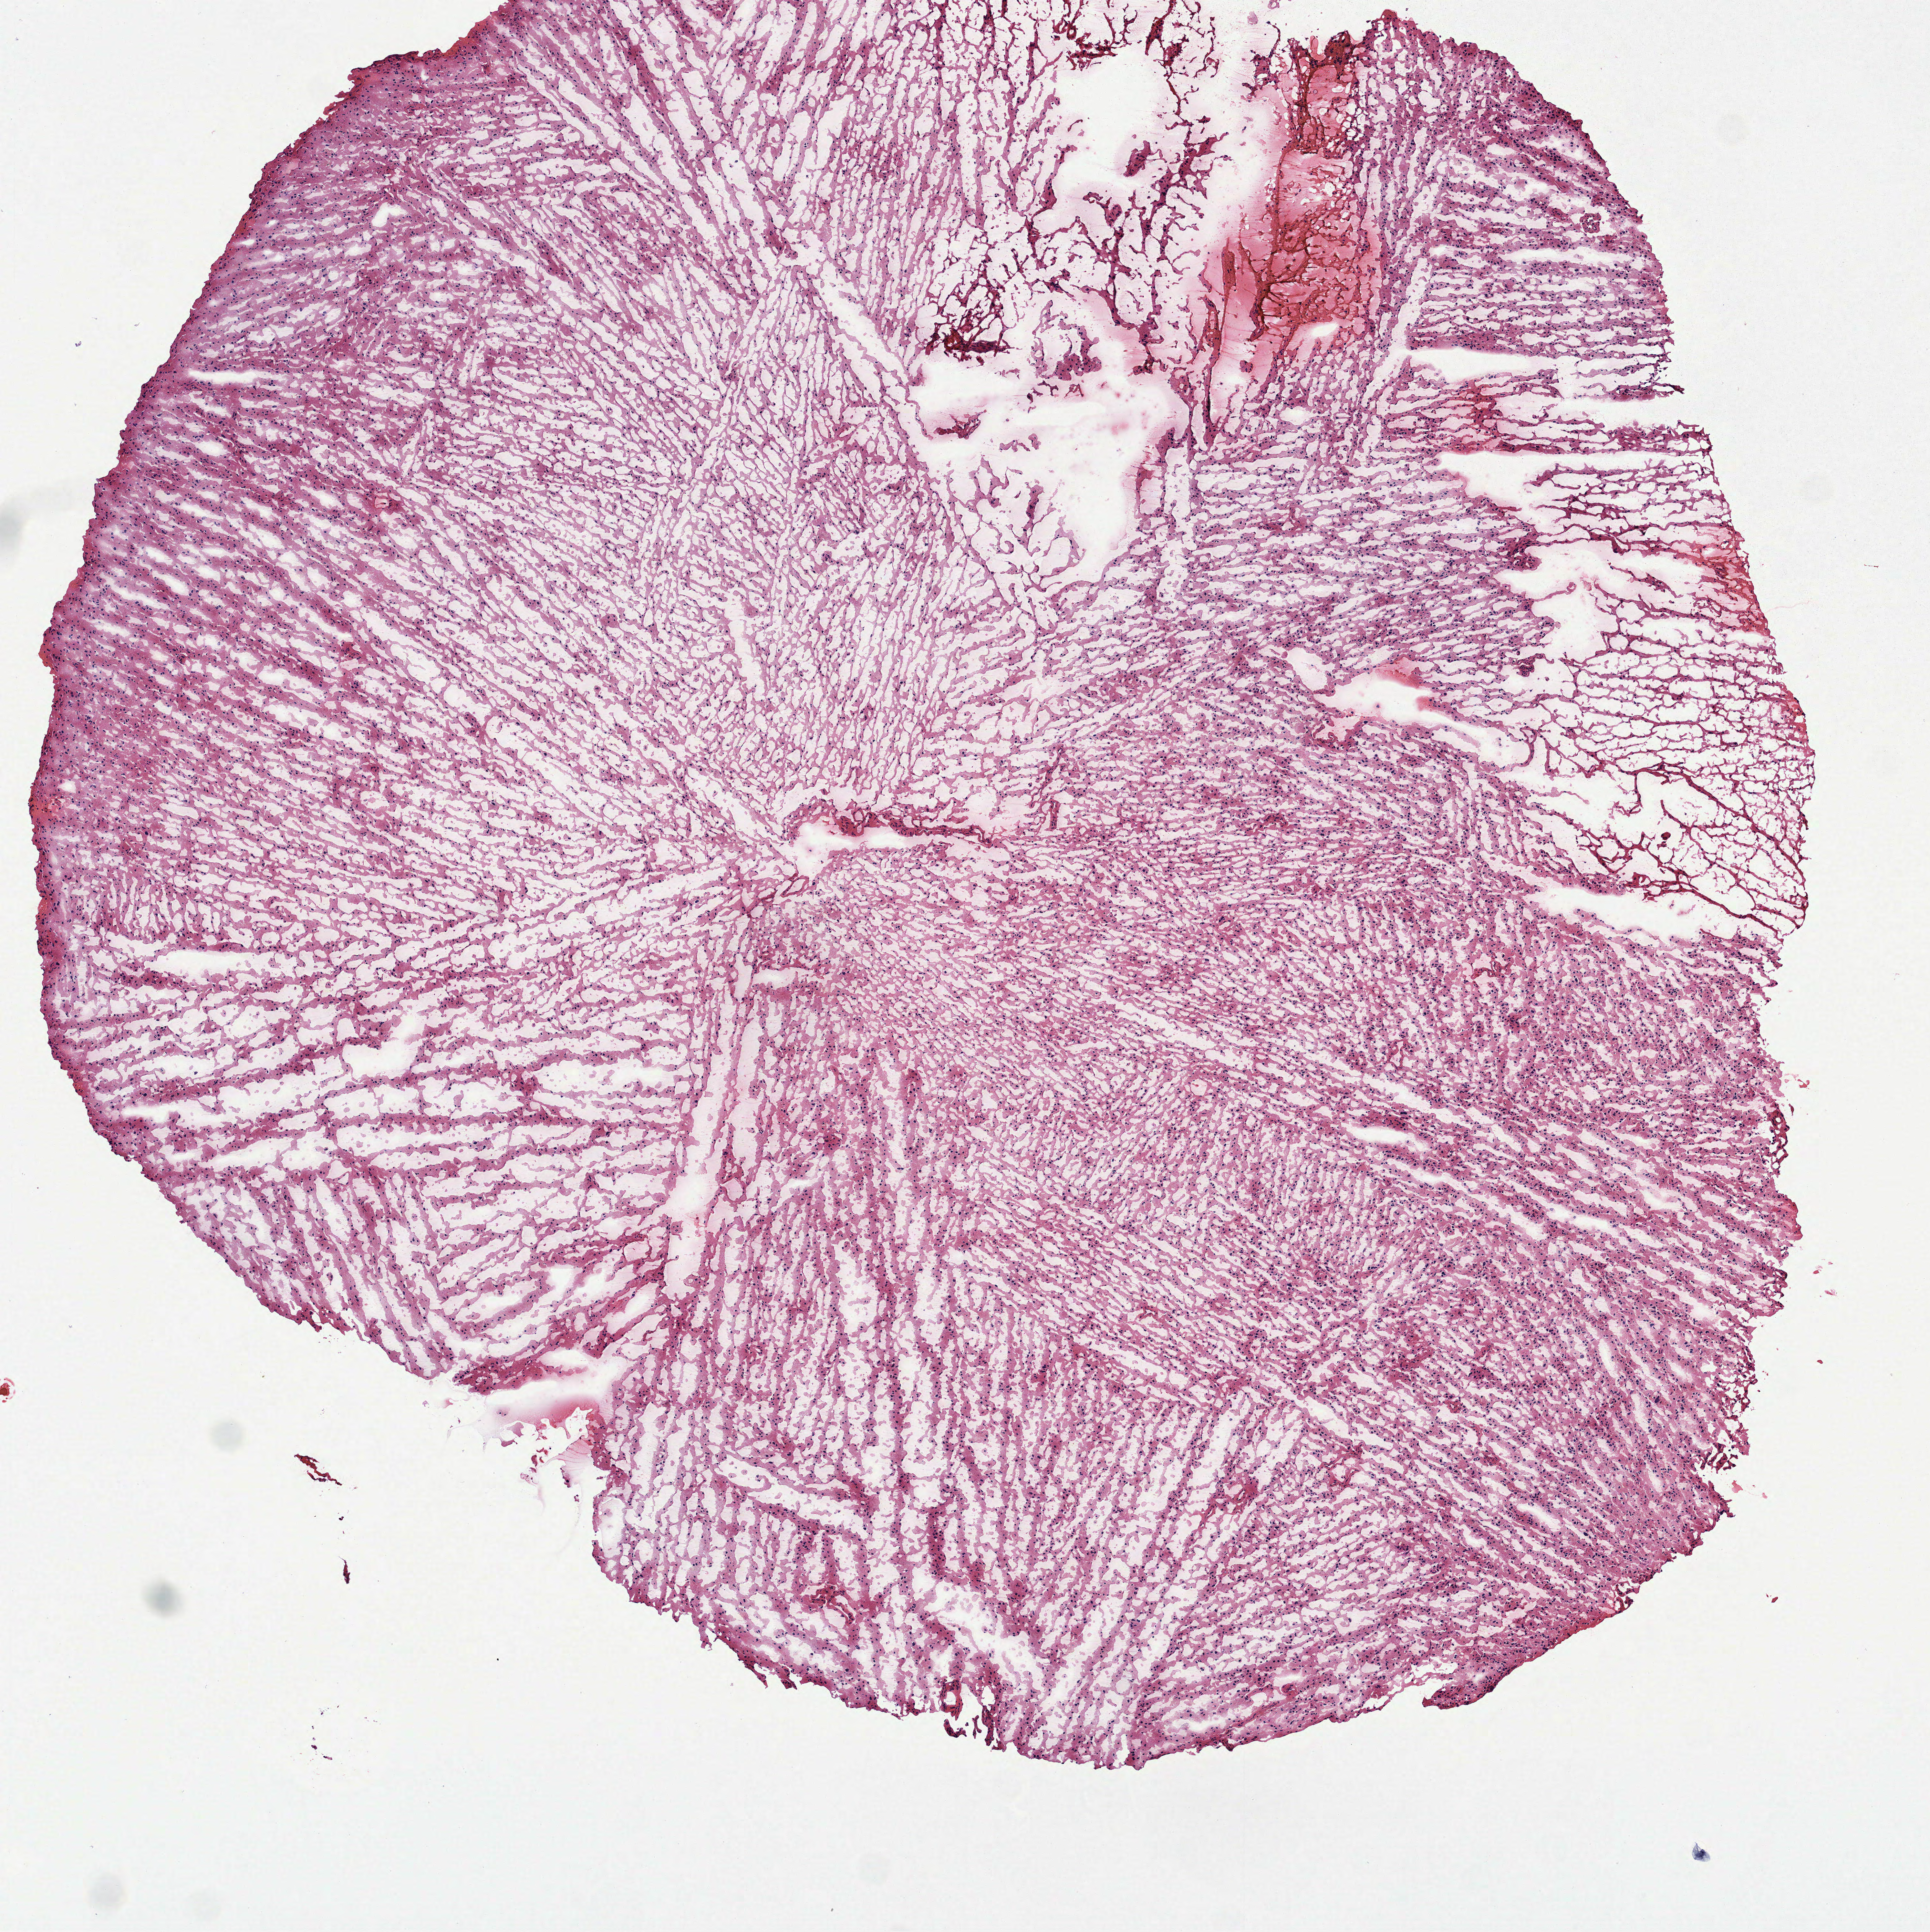
Digitized H&E tissue section (whole slide) — shown as a low-resolution overview of the whole scanned area (about 6.0 x 6.0 mm, slide scanned at 40x); frozen section; sample: primary tumour, brain. Female, age 39 years at initial diagnosis. Histologic grade: G2 (moderately differentiated). Pathologist review of this section (percent, as recorded): tumour cells 100%, tumour nuclei 70%, normal cells 0%, stromal cells 0%, necrosis 0%.
Histologic diagnosis: Astrocytoma, NOS.